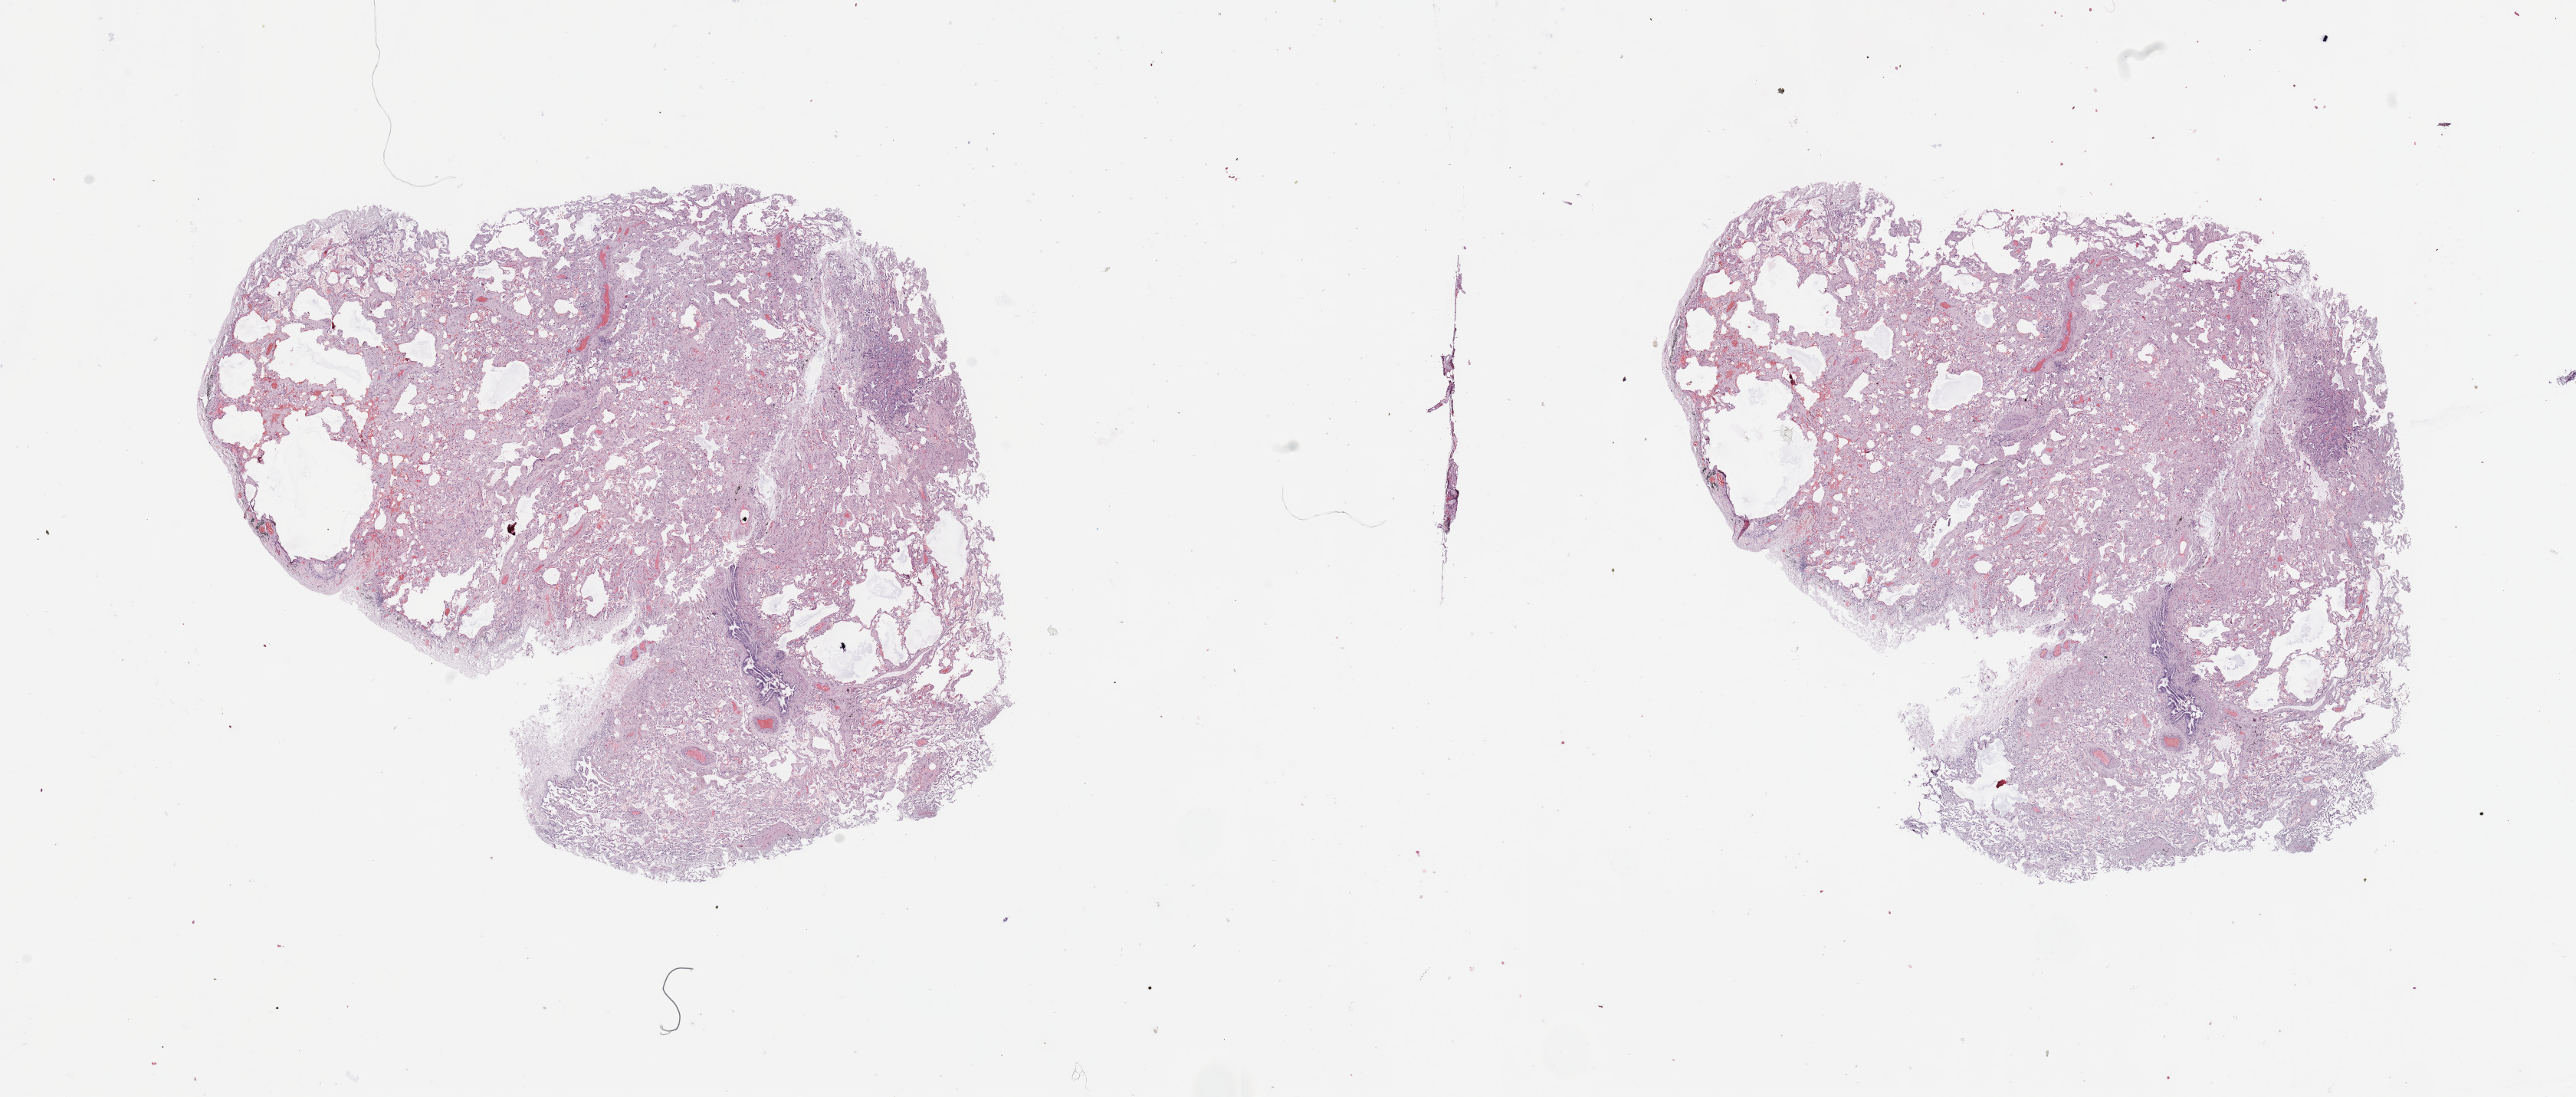
Hematoxylin and eosin (H&E) stained whole-slide image, whole scanned area (about 26.6 x 11.3 mm, from a 20x scan) shown as a low-resolution overview; normal (non-tumour) tissue sample, lung. Patient: male, age 72 years.
This section: normal (non-tumour) tissue from the same patient. Patient diagnosis: Squamous cell carcinoma, NOS.